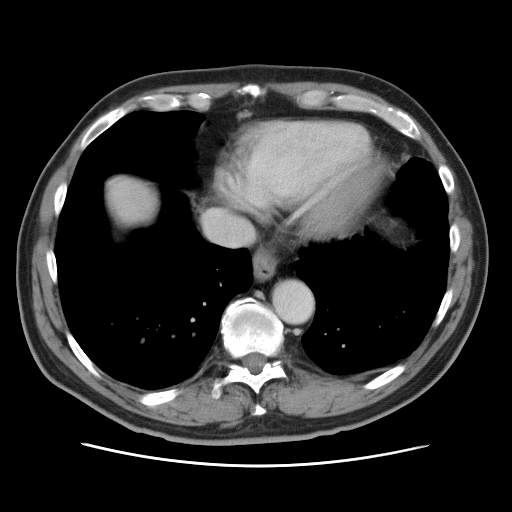
Contrast-enhanced abdominal CT, one axial slice; slice 74 of 80 in the series (ordered by position); 120 kVp; intravenous contrast given; soft-tissue window (W 400 / L 40 HU); 512 × 512 image matrix, field of view 370 × 370 mm. Male patient, age 69 years. Case-level facts recorded for this patient, not image findings: diagnosis: colorectal cancer liver metastases, imaged before liver resection; multiple liver metastases: no.
Outlined on this slice (manually delineated by an expert):
- hepatic veins: bounding box (x1, y1, x2, y2) in pixels: (205, 210, 252, 246)
- liver: (107, 178, 157, 225)
- planned liver remnant (the part of the liver to remain after resection): (133, 219, 141, 223)